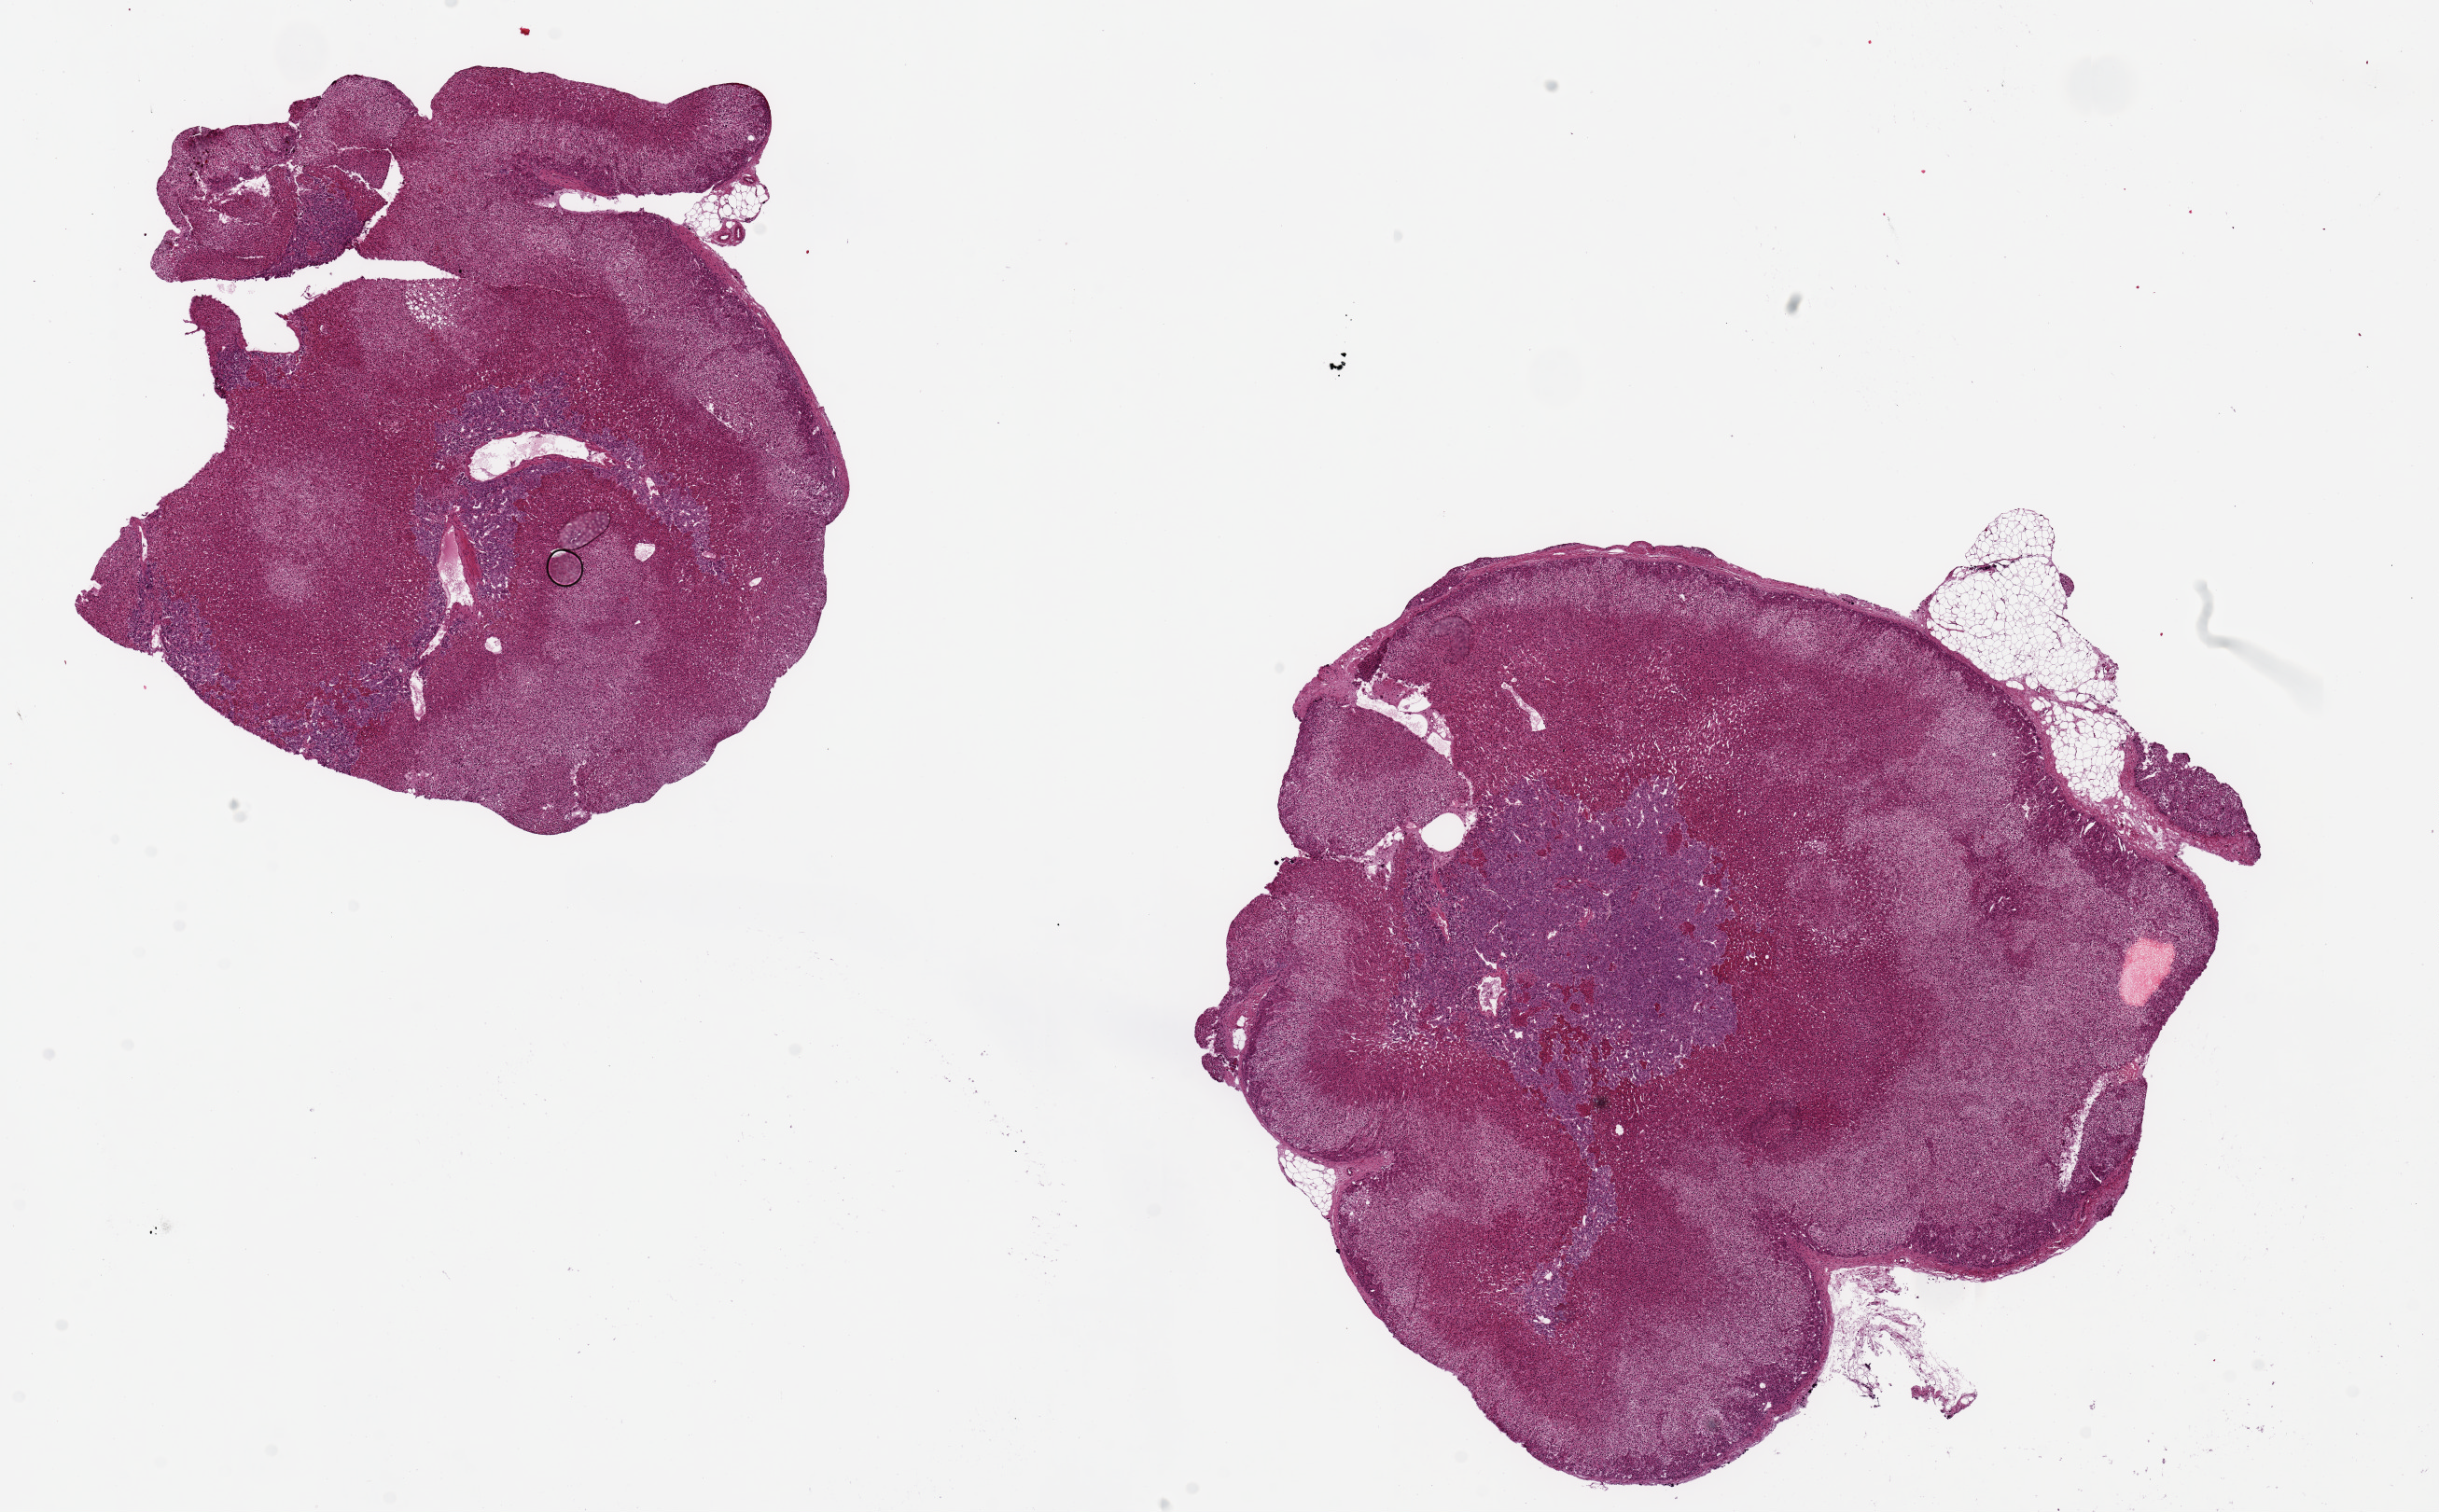
Hematoxylin and eosin (H&E) whole-slide image, a low-resolution overview of the entire scanned area, about 20.7 x 12.8 mm, PAXgene-fixed paraffin-embedded (PFPE) section, target tissue: adrenal gland, donor tissue sample. Donor: male.
* pathologist's review note for this sample: 2 pieces ~7x6mm. Central foci of medulla in both 2-2.5mm in d. All extremely well preserved